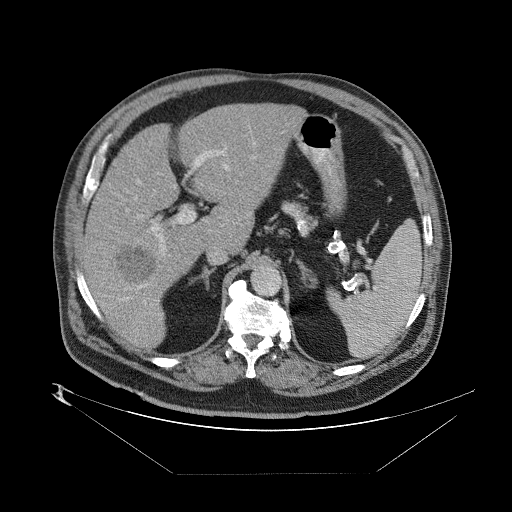
Contrast-enhanced abdominal CT (liver protocol), one axial slice; reconstruction kernel STANDARD; 140 kVp; one of 2 acquisitions stored at this slice position; soft-tissue window (W 400 / L 40 HU); 2.5 mm slice thickness; 512 × 512 image matrix, field of view 480 × 480 mm. Case-level facts recorded for this patient, not image findings: diagnosis: hepatocellular carcinoma (patient treated with transarterial chemoembolisation; whether this scan precedes or follows treatment is not stated here); TNM stage (as recorded): Stage-II; Child-Pugh class: B; tumour differentiation: moderately differentiated; tumour size: 4 cm.
Outlined on this slice (semi-automatic segmentation, software-assisted and operator-edited):
- abdominal aorta: bounding box <252,265,280,294> (left, top, right, bottom; pixels)
- liver parenchyma outside the tumour (the mass and vessels are separate outlines, so this box may not span the whole liver): <84,100,298,348>
- mass: <112,242,157,289>
- liver vessels: <85,134,255,289>